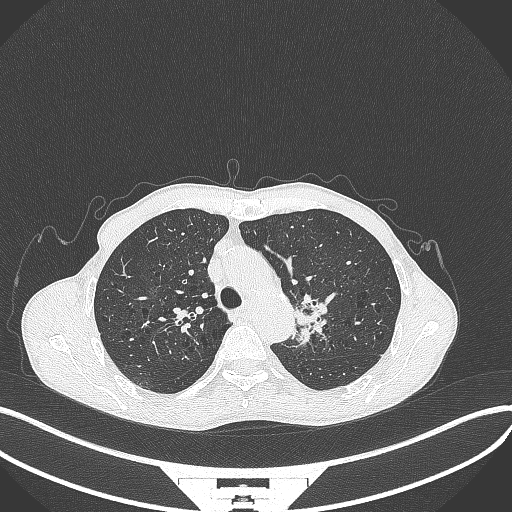
Chest CT, one axial slice. Reconstruction kernel B70f. Lung window (W 1500 / L -600 HU). 1 mm slice thickness. 512 × 512 image matrix, field of view 400 × 400 mm. Patient: male, 65 years. Case-level facts recorded for this patient, not image findings: clinical TNM (as recorded): T2b N0 M0; histopathological grade: G2.
Structures marked on this image (rectangle marked by the reading radiologist):
- lung tumour (recorded histology: adenocarcinoma): bounding box <290,292,331,350> (left, top, right, bottom; pixels)